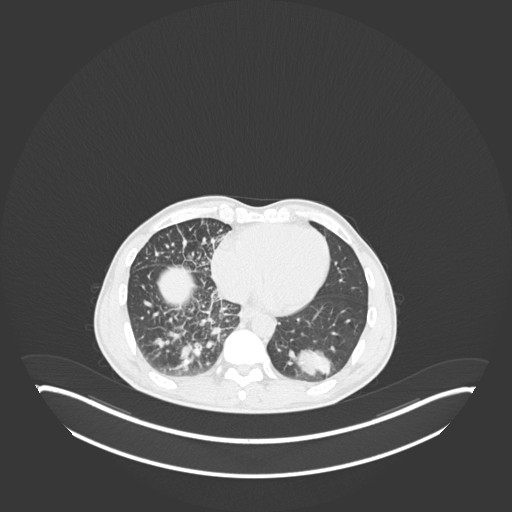
Chest CT, one axial slice; position 71 of 237 along the scan axis; 120 kVp; lung window (W 1500 / L -600 HU); 1 mm slice thickness; 512 × 512 image matrix, field of view 500 × 500 mm. Male patient, age 49 years. Case-level facts recorded for this patient, not image findings: clinical TNM (as recorded): T2b N1 M0.
Annotated regions visible in this slice (bounding box drawn by a radiologist):
- lung tumour (recorded histology: adenocarcinoma): bounding box <290,343,337,378> (left, top, right, bottom; pixels)